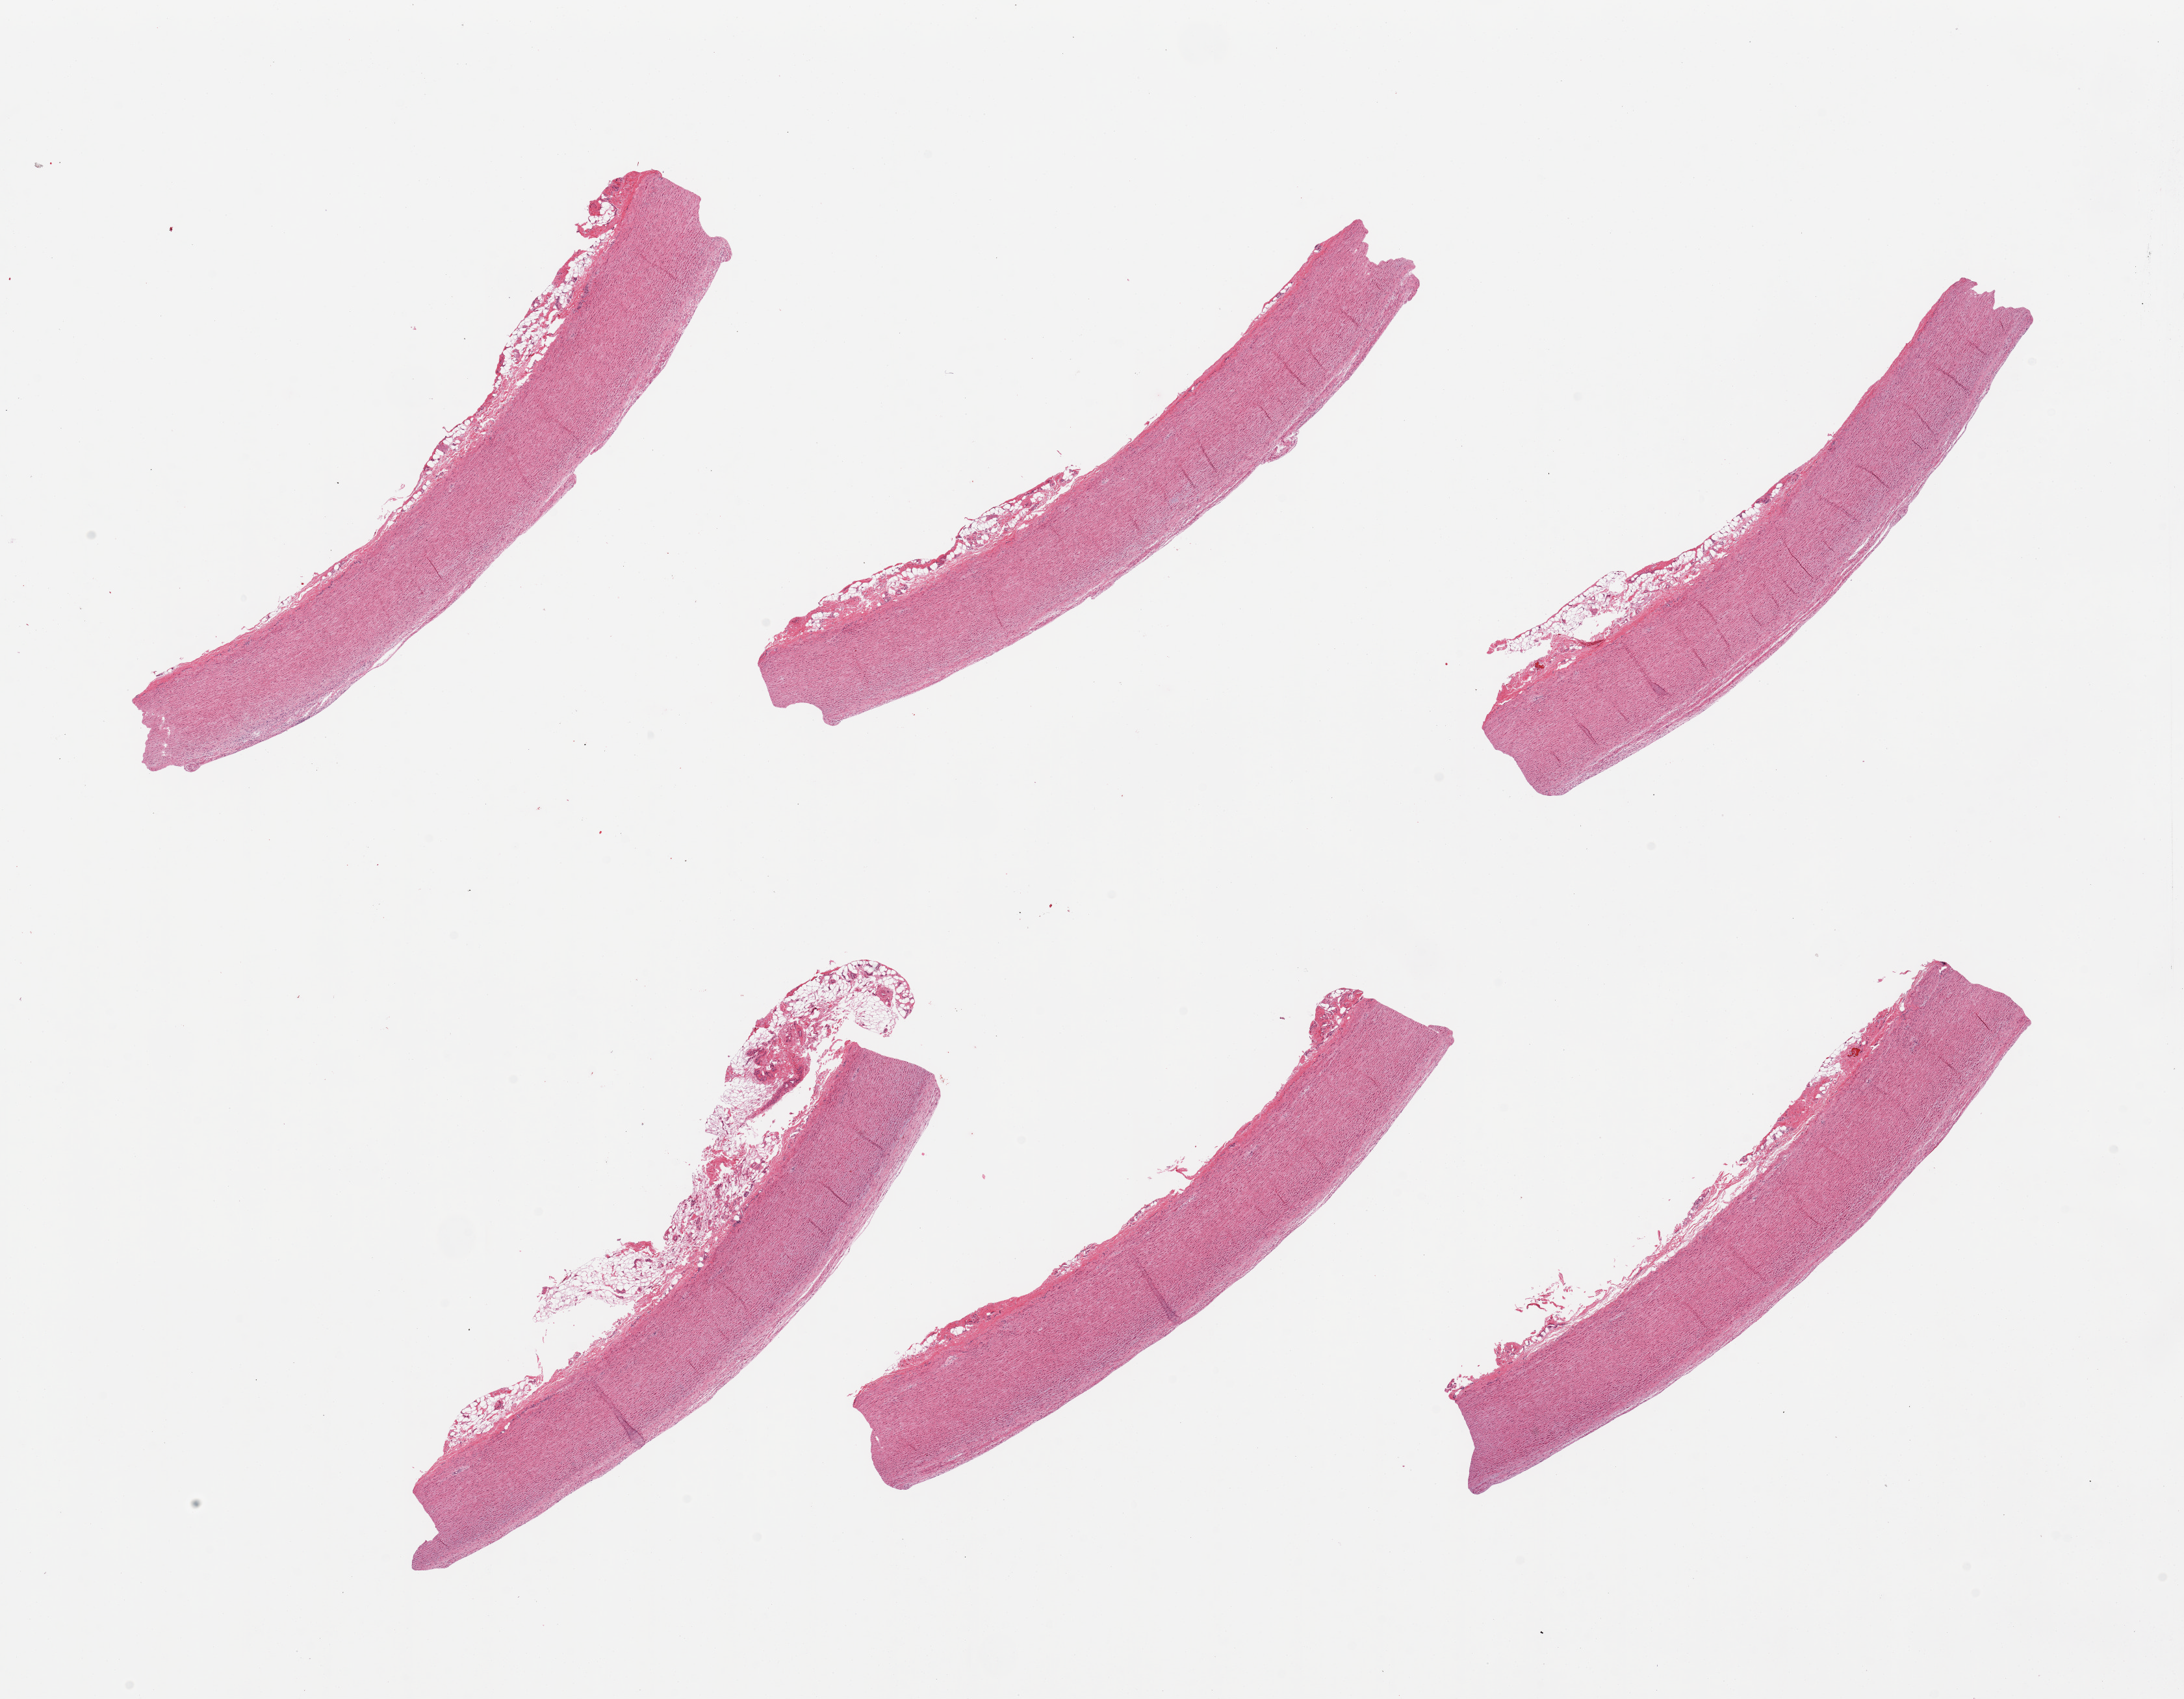
Haematoxylin and eosin whole-slide image — a low-resolution overview of the entire scanned area, about 26.6 x 20.7 mm (acquisition: 20x scan), PAXgene-fixed, paraffin-embedded tissue, section of aorta (target tissue), donor tissue sample. Male donor.
- pathologist's review note for this sample: 6 pieces, up to ~1mm adherent serosa on several sections